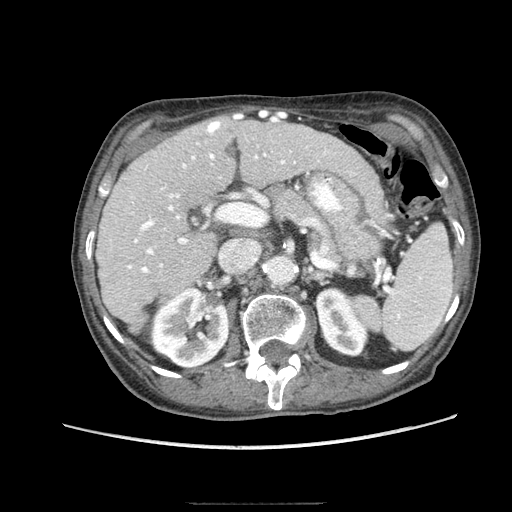
Contrast-enhanced abdominal CT (liver protocol), one axial slice. Slice 46 of 83 in the series (ordered by position). 140 kVp. Soft-tissue window (W 400 / L 40 HU). 2.5 mm slice thickness. 512 × 512 image matrix, field of view 360 × 360 mm. From the clinical record (not read from this slice): diagnosis: hepatocellular carcinoma (patient treated with transarterial chemoembolisation; whether this scan precedes or follows treatment is not stated here); TNM stage (as recorded): Stage-I; Child-Pugh class: A; tumour differentiation: moderately differentiated; tumour nodularity: uninodular.
Structures marked on this image (semi-automatic segmentation, software-assisted and operator-edited):
- liver parenchyma outside the tumour (the mass and vessels are separate outlines, so this box may not span the whole liver): bounding box [x1, y1, x2, y2] px = [96, 116, 342, 332]
- liver vessels: [127, 116, 328, 273]